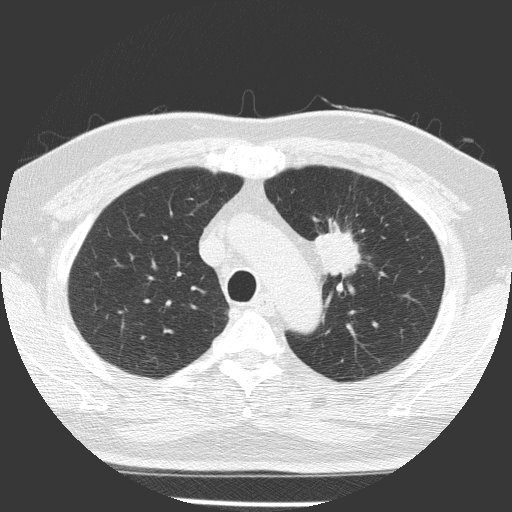
Chest CT (low-dose screening protocol), one axial image, first (baseline) screen, lung window (W 1500 / L -600 HU), 2 mm slice thickness, lung (sharp) reconstruction kernel (FC51). Male, age 70 years at enrolment. Current smoker at enrolment.
- Lesion marked by an expert reader, bounding box [x1, y1, x2, y2] px = [298, 222, 372, 296].
- The screening reader recorded 3 non-calcified nodules or masses ≥4 mm on this exam; which of them this box marks is not recorded.
- Later outcome: lung cancer diagnosed 58 days after this screen — squamous cell carcinoma, NOS, left upper lobe, poorly differentiated (G3), stage IB (AJCC 6th edition), 47 mm at pathology.